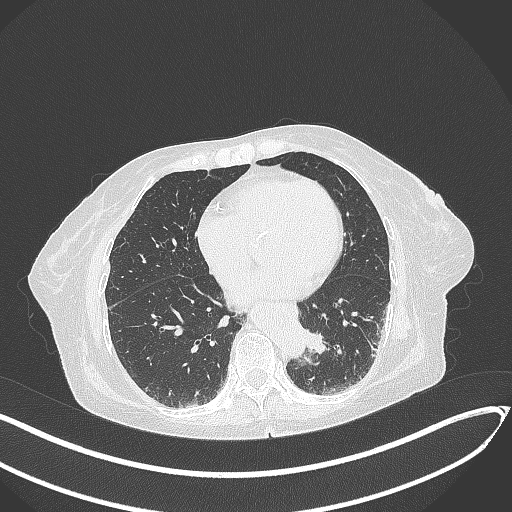
Chest CT, one axial slice. Position 79 of 324 along the scan axis. Reconstruction kernel B70f. 120 kVp. Lung window (W 1500 / L -600 HU). 1 mm slice thickness. 512 × 512 image matrix. Female patient, age 82 years. From the clinical record (not read from this slice): clinical TNM (as recorded): T1b N0 M1.
Annotated regions visible in this slice (rectangle marked by the reading radiologist):
- lung tumour (recorded histology: adenocarcinoma): bounding box (x1, y1, x2, y2) in pixels: (299, 325, 331, 361)